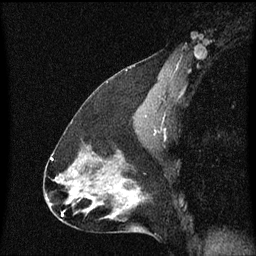
Breast MRI (dynamic contrast-enhanced), one sagittal slice. Position 38 of 60 along the scan axis. Dynamic contrast-enhanced series, image 2 of 3 at this slice position (ordered by acquisition). 1.5 T. TE 4.2 ms, TR 8.4 ms. 2 mm slice thickness. 256 × 256 image matrix. Patient: female, 47 years.
Annotated regions visible in this slice (semi-automatically segmented with operator editing):
- analysis volume of interest (the breast-tissue region the enhancement analysis was run in; not a lesion): box from (x=100, y=172) to (x=144, y=219) px
- tumour enhancement mask (voxels above the 70 % enhancement threshold inside the analysis volume of interest): (x=121, y=184)–(x=136, y=207)